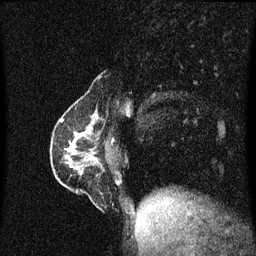
Breast MRI (dynamic contrast-enhanced), one sagittal slice; position 19 of 60 along the scan axis; dynamic contrast-enhanced series, image 2 of 3 at this slice position (ordered by acquisition); 1.5 T; TE 4.2 ms, TR 8.4 ms; 2 mm slice thickness; 256 × 256 image matrix. Female patient, age 40 years.
Annotated regions visible in this slice (semi-automatic segmentation, software-assisted and operator-edited):
- analysis volume of interest (the breast-tissue region the enhancement analysis was run in; not a lesion): bounding box <57,110,111,189> (left, top, right, bottom; pixels)
- tumour enhancement mask (voxels above the 70 % enhancement threshold inside the analysis volume of interest): <61,116,97,165>